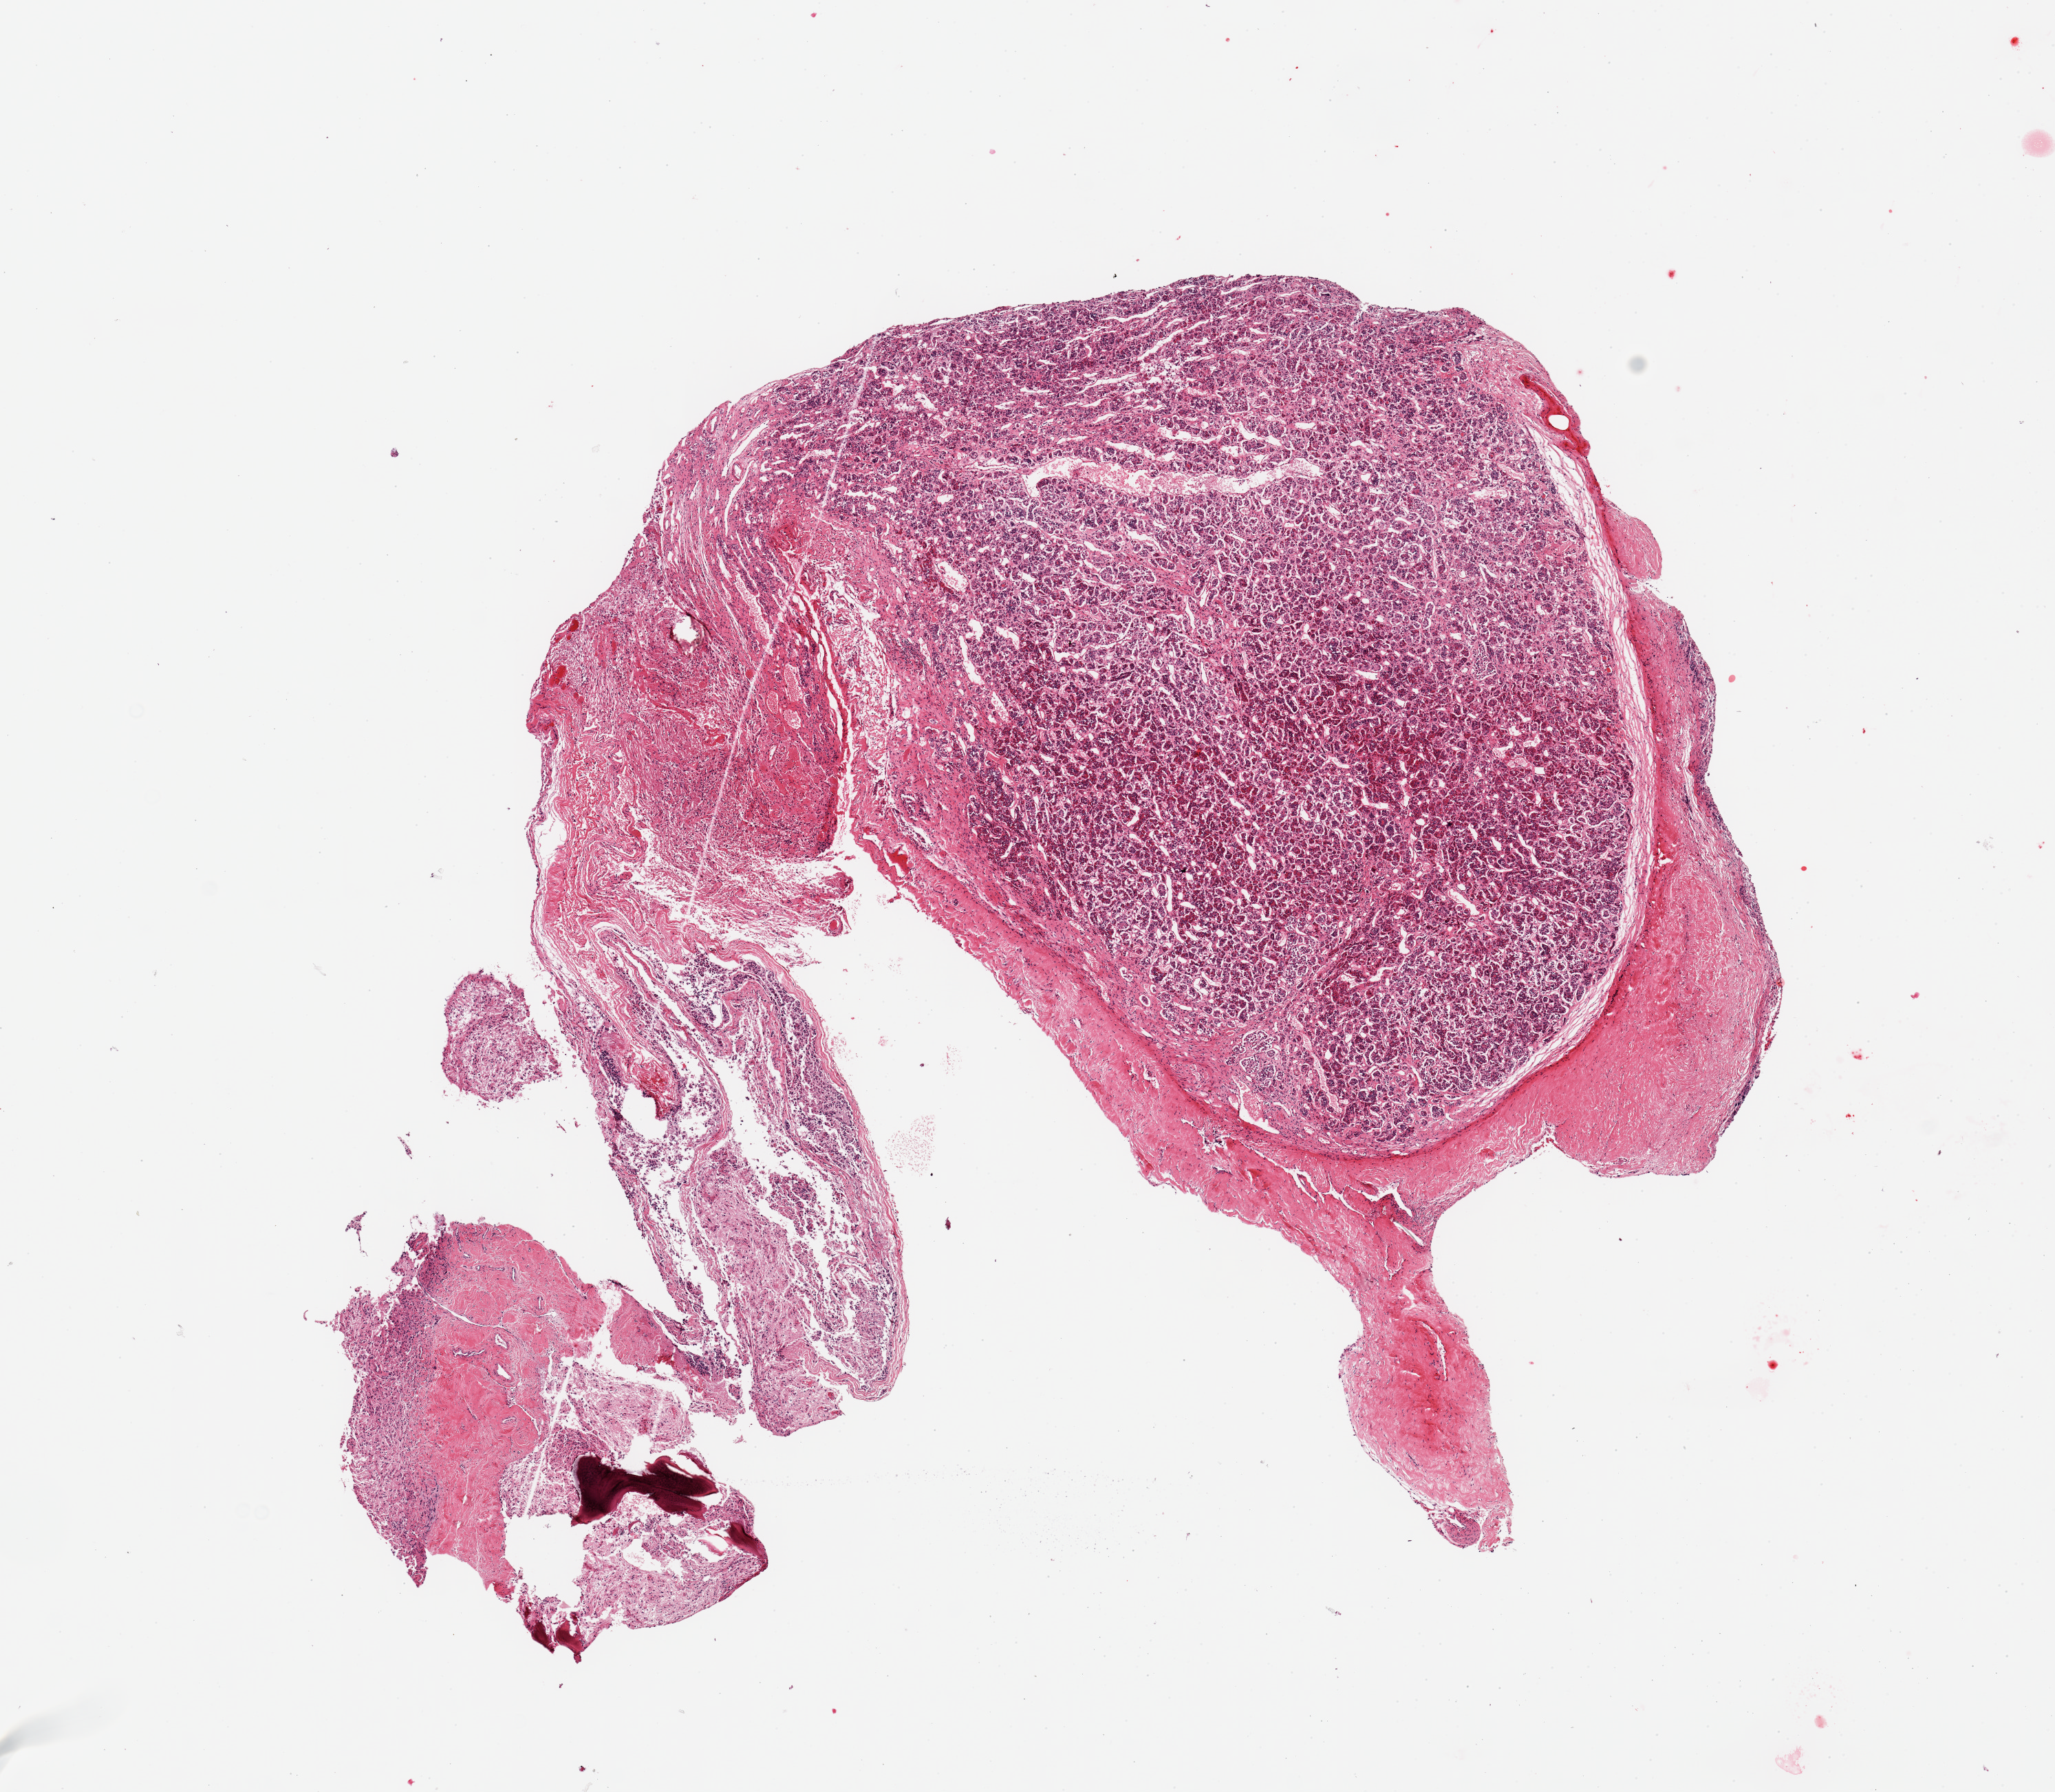
Whole-slide image, haematoxylin and eosin stain, brightfield — a low-resolution overview of the entire scanned area, about 11.8 x 10.3 mm (from a 20x scan). PAXgene-fixed, paraffin-embedded tissue. Section of pituitary (target tissue). Tissue donor sample. Donor: male.
Pathologist's review note for this sample: 1 piece, ~20% neurohypophysis; rest is adenohypophysis; focal dural elements/bone.